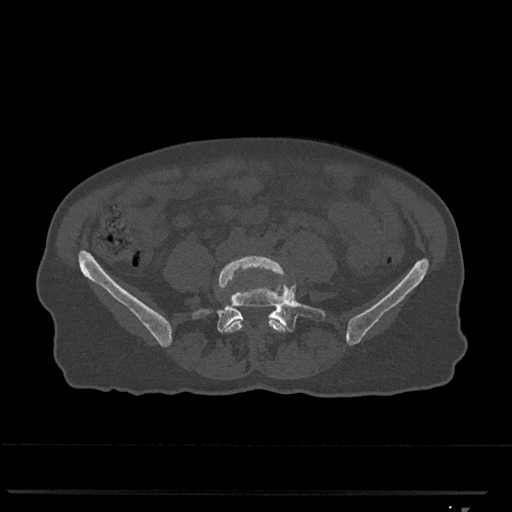
CT including the spine, one axial slice; slice 173 of 793 in the series (ordered by position); reconstruction kernel Br40s/3; bone window (W 1800 / L 400 HU); 0.5 mm slice thickness; 512 × 512 image matrix, field of view 380 × 380 mm. Female patient, age 62 years. From the clinical record (not read from this slice): primary cancer: renal.
Structures marked on this image (semi-automatic segmentation, software-assisted and operator-edited):
- L4 vertebra: box from (x=218, y=255) to (x=287, y=333) px
- L5 vertebra: (x=192, y=260)–(x=326, y=333)